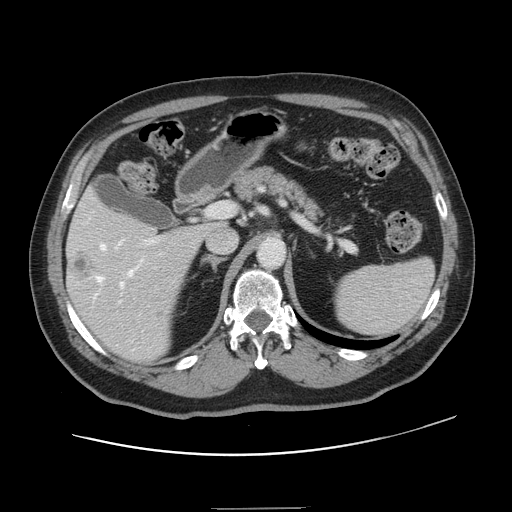
Contrast-enhanced abdominal CT, one axial slice; slice 84 of 143 in the series (ordered by position); intravenous contrast given; soft-tissue window (W 400 / L 40 HU); 2.5 mm slice thickness; 512 × 512 image matrix. Male patient, age 62 years. From the clinical record (not read from this slice): diagnosis: colorectal cancer liver metastases, imaged before liver resection; multiple liver metastases: yes; largest metastasis: 2.7 cm; disease in both lobes: no.
Structures marked on this image (outlined manually by an expert reader):
- hepatic veins: bounding box (x1, y1, x2, y2) in pixels: (94, 245, 142, 299)
- liver: (67, 193, 212, 362)
- planned liver remnant (the part of the liver to remain after resection): (70, 192, 216, 239)
- portal vein (with intrahepatic branches): (119, 205, 220, 303)
- liver metastasis: (70, 253, 95, 281)